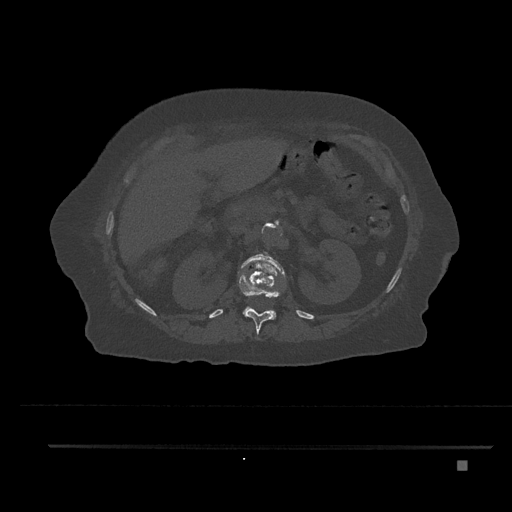
CT including the spine, one axial slice; position 247 of 797 along the scan axis; reconstruction kernel Br40s/3; 120 kVp; bone window (W 1800 / L 400 HU); 0.5 mm slice thickness; 512 × 512 image matrix, field of view 437 × 437 mm. Patient: female, 76 years. Case-level facts recorded for this patient, not image findings: primary cancer: lung; vertebrae with lytic lesions (as recorded): T11, L3.
Structures marked on this image (semi-automatic segmentation, software-assisted and operator-edited):
- L1 vertebra: box from (x=240, y=254) to (x=285, y=320) px
- T12 vertebra: (x=239, y=270)–(x=282, y=334)